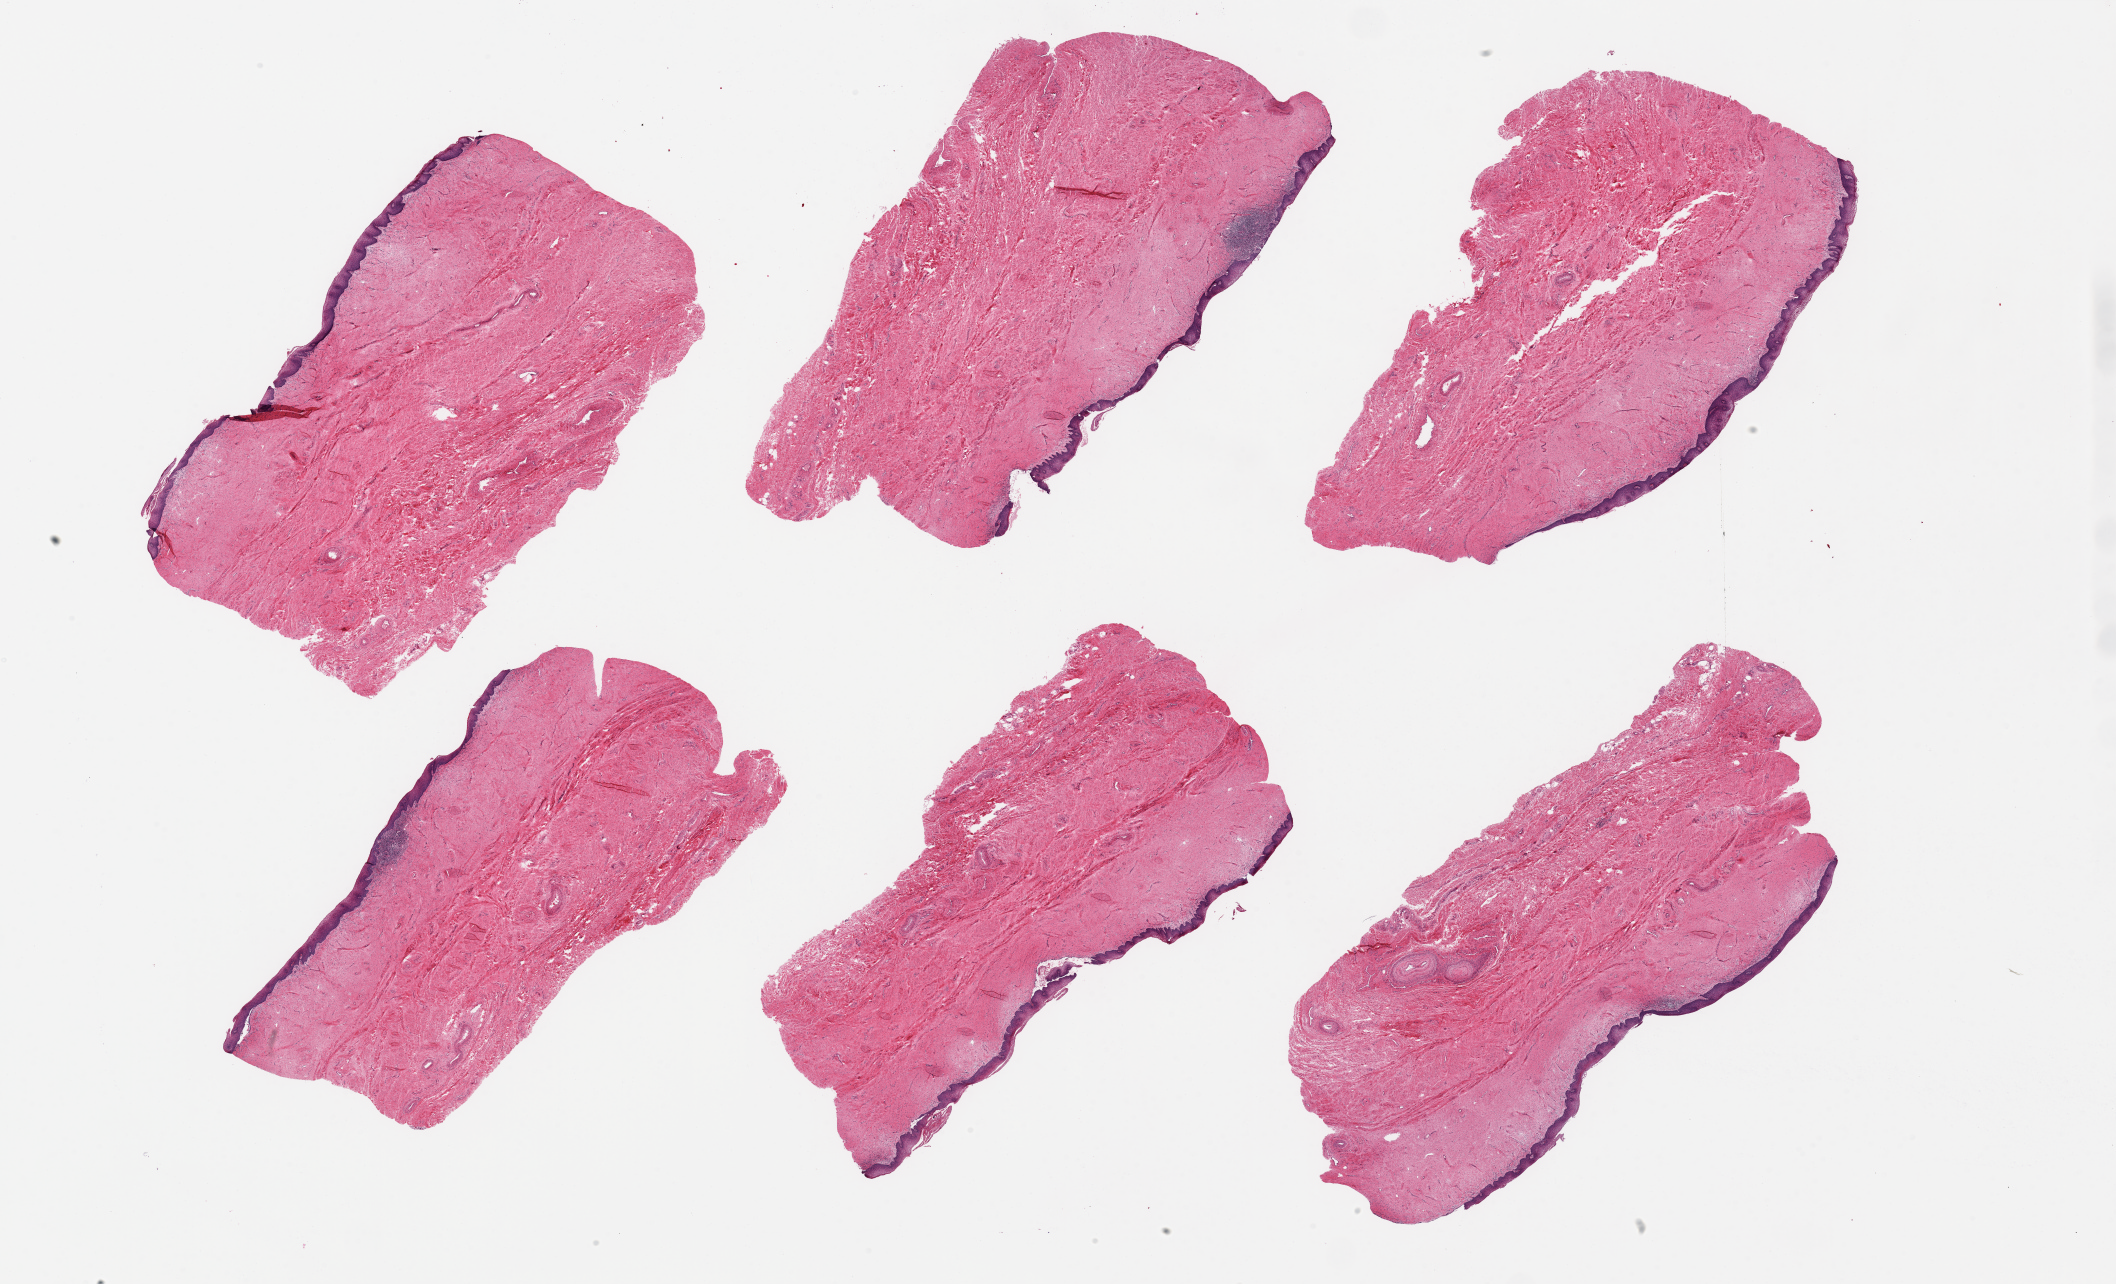
Haematoxylin and eosin whole-slide image — shown as a low-resolution overview of the whole scanned area (about 33.5 x 20.3 mm, slide scanned at 20x), PAXgene-fixed, paraffin-embedded tissue, target tissue: vagina, tissue donor sample. Donor sex: female.
Reviewer comment on this tissue sample: 6 pieces; few lymphoid aggregates.